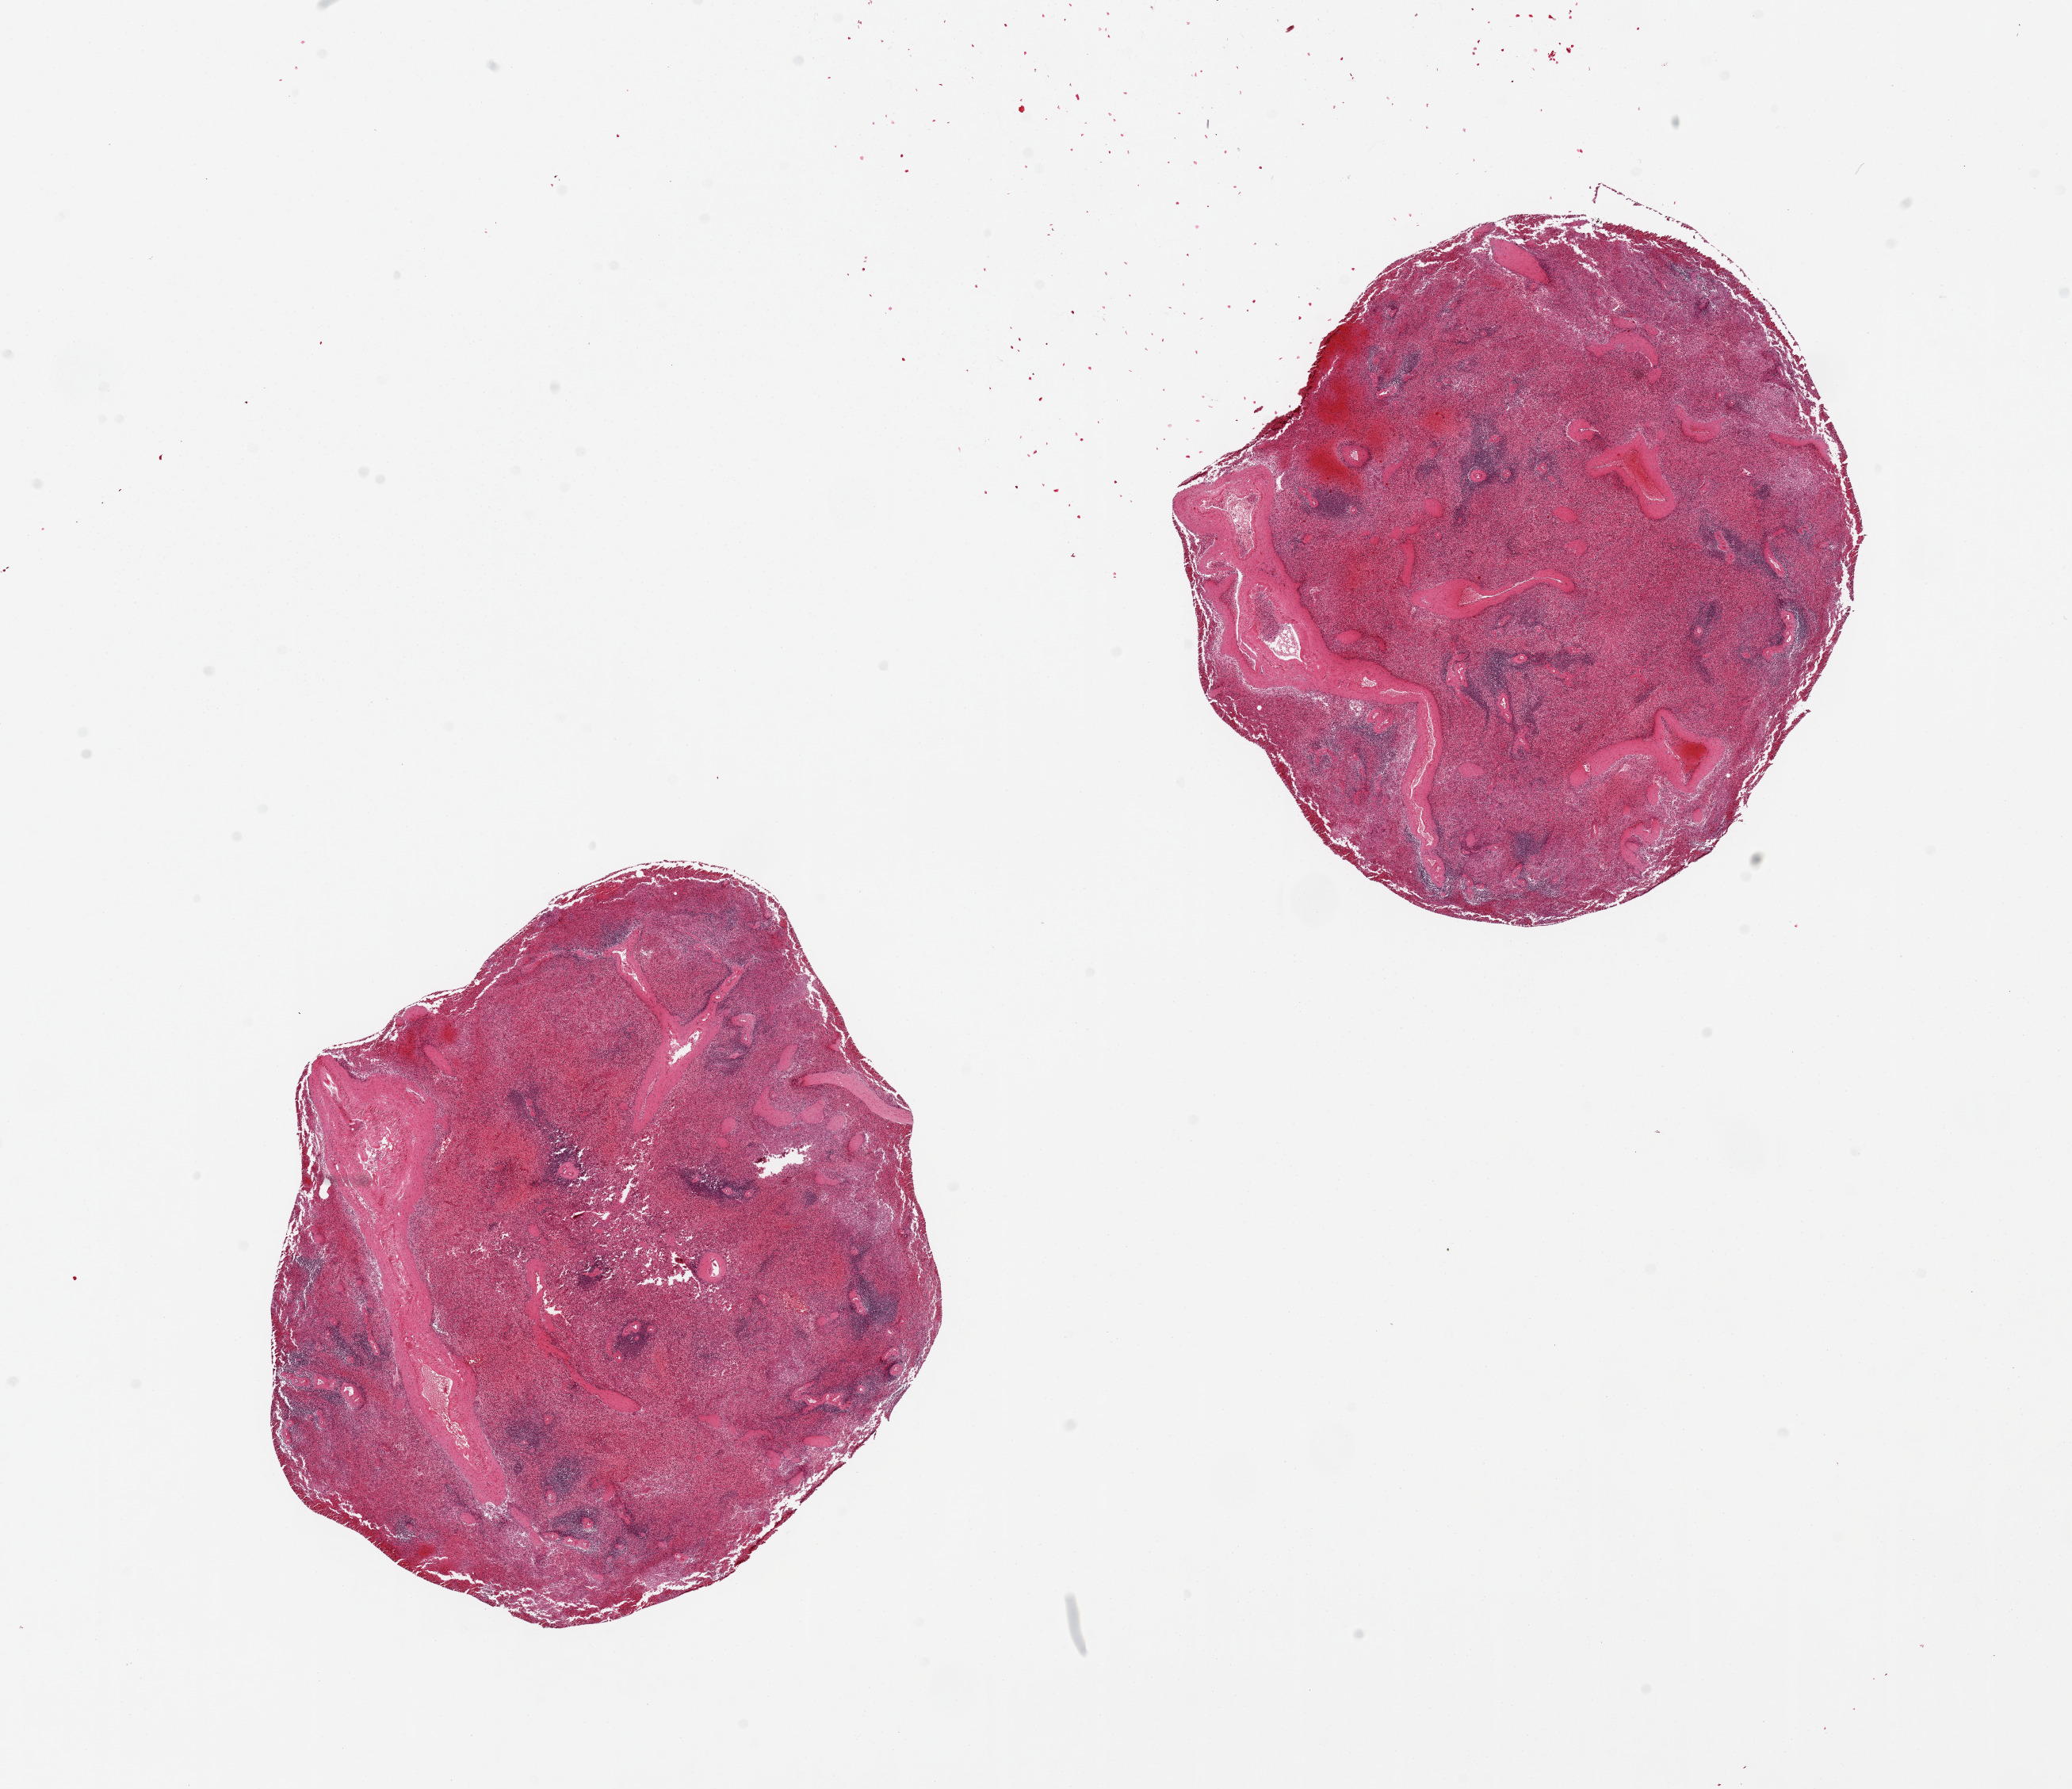
Whole-slide image, haematoxylin and eosin stain, a low-resolution overview of the entire scanned area, about 20.7 x 17.8 mm (slide scanned at 20x); PAXgene-fixed, paraffin-embedded tissue; section of spleen (target tissue); tissue donor sample. Donor sex: male.
Review note (as recorded): 2 pieces, moderate congestion, badly autolyzed.